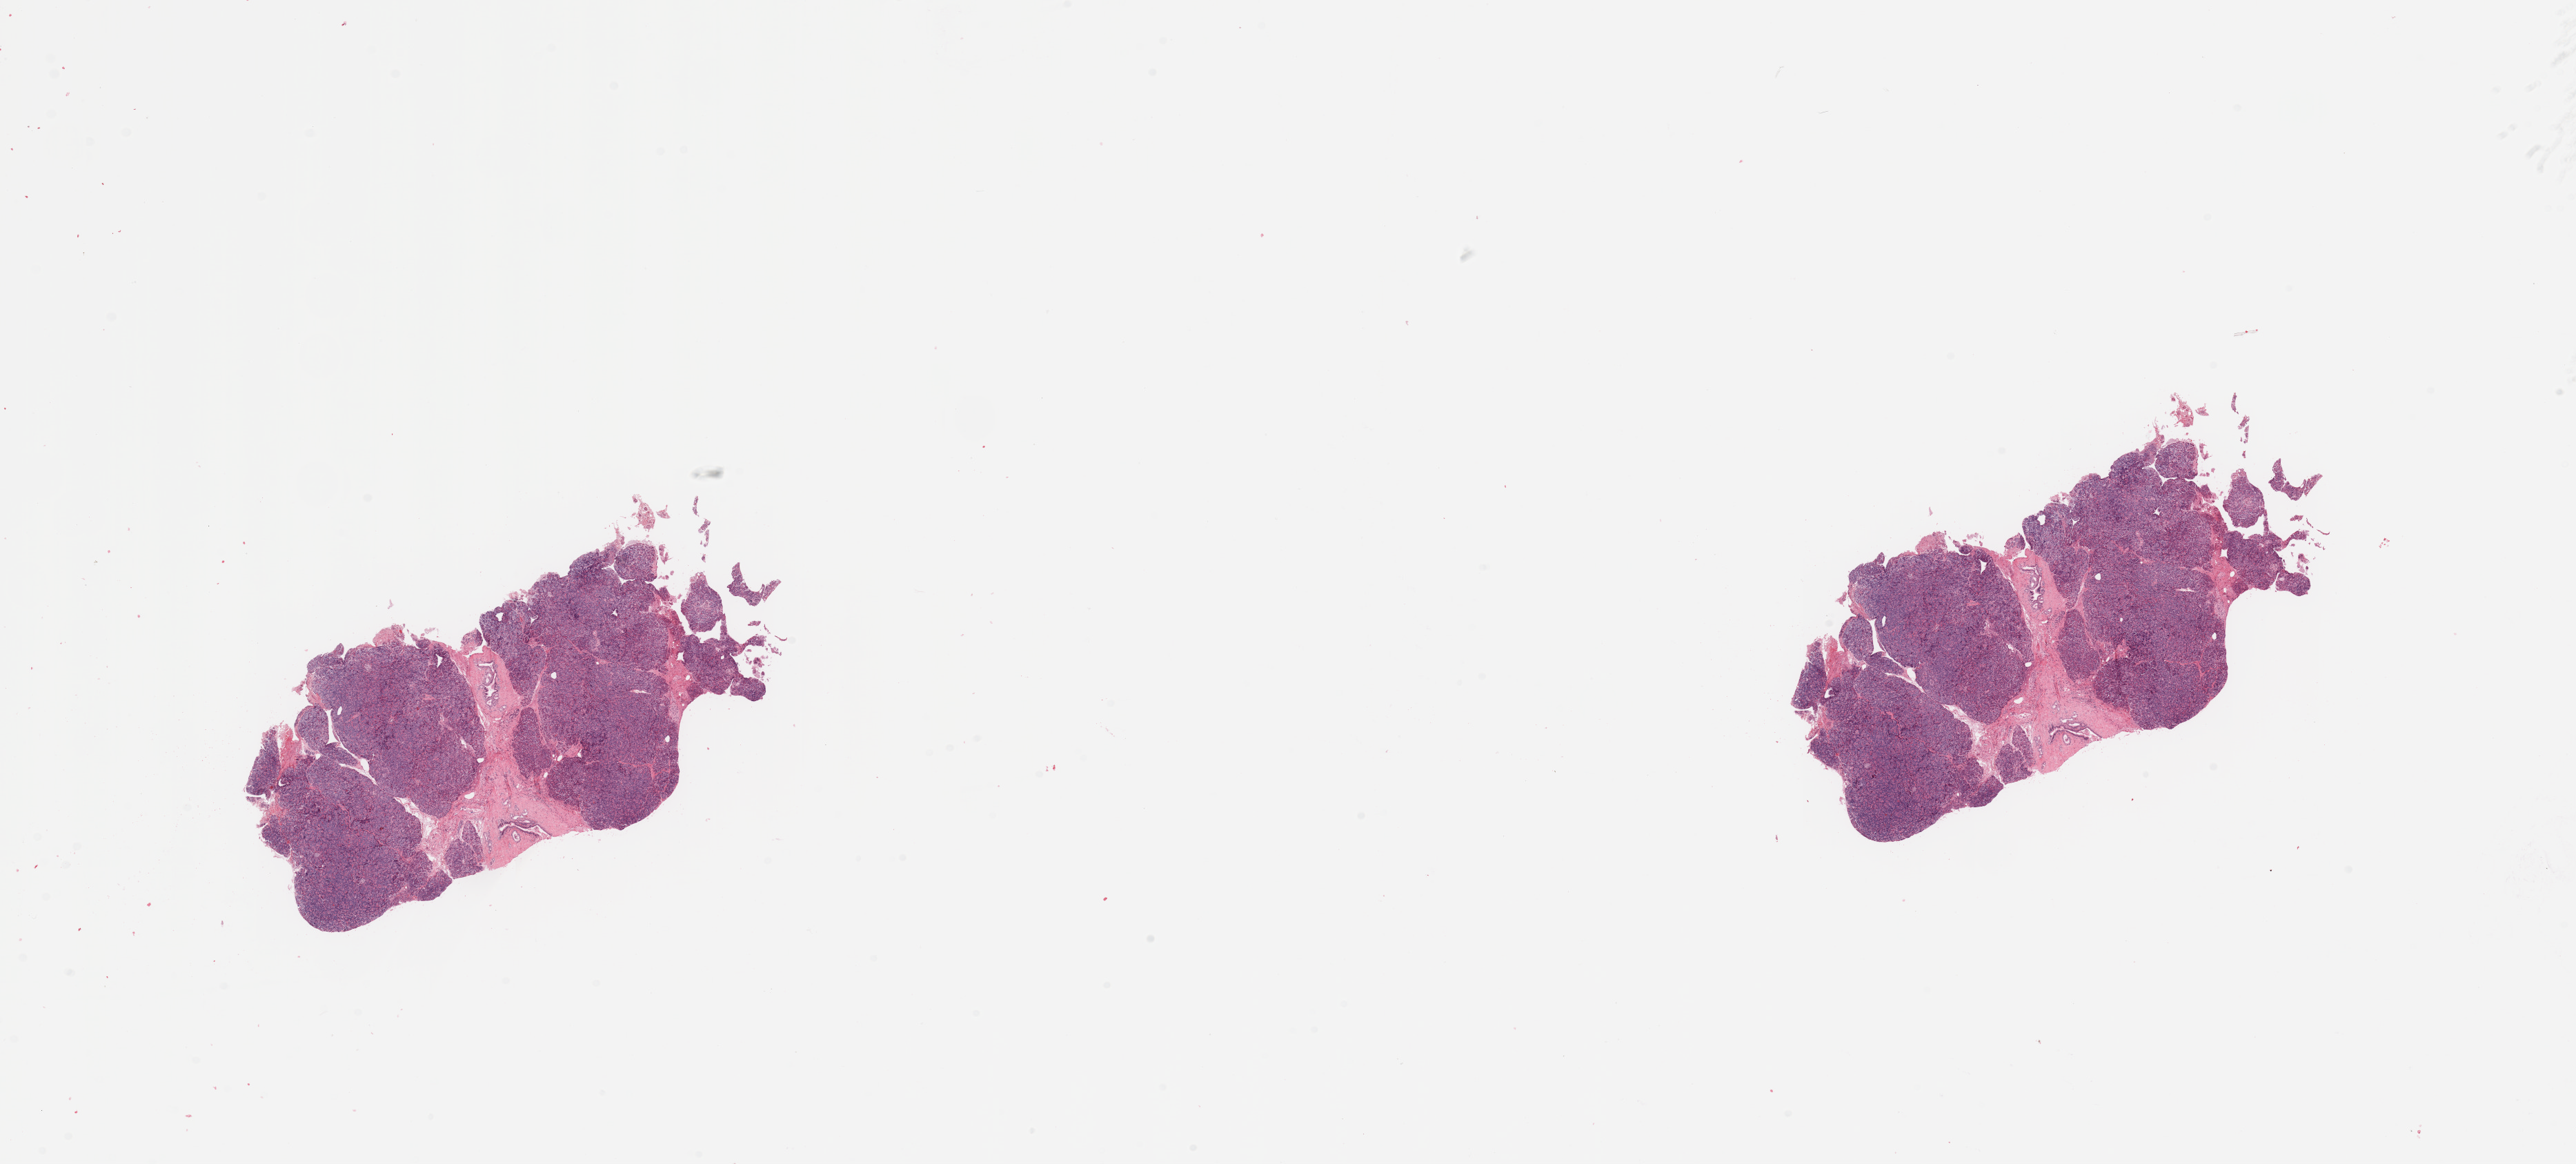
Whole-slide histology image, Hematoxylin and eosin (H&E) stained, shown as a low-resolution overview of the whole scanned area (about 29.5 x 13.3 mm, slide scanned at 20x), normal (non-tumour) tissue sample, pancreas. Male, 71 y/o.
This section: normal (non-tumour) tissue from the same patient. Patient diagnosis: Infiltrating duct carcinoma, NOS.